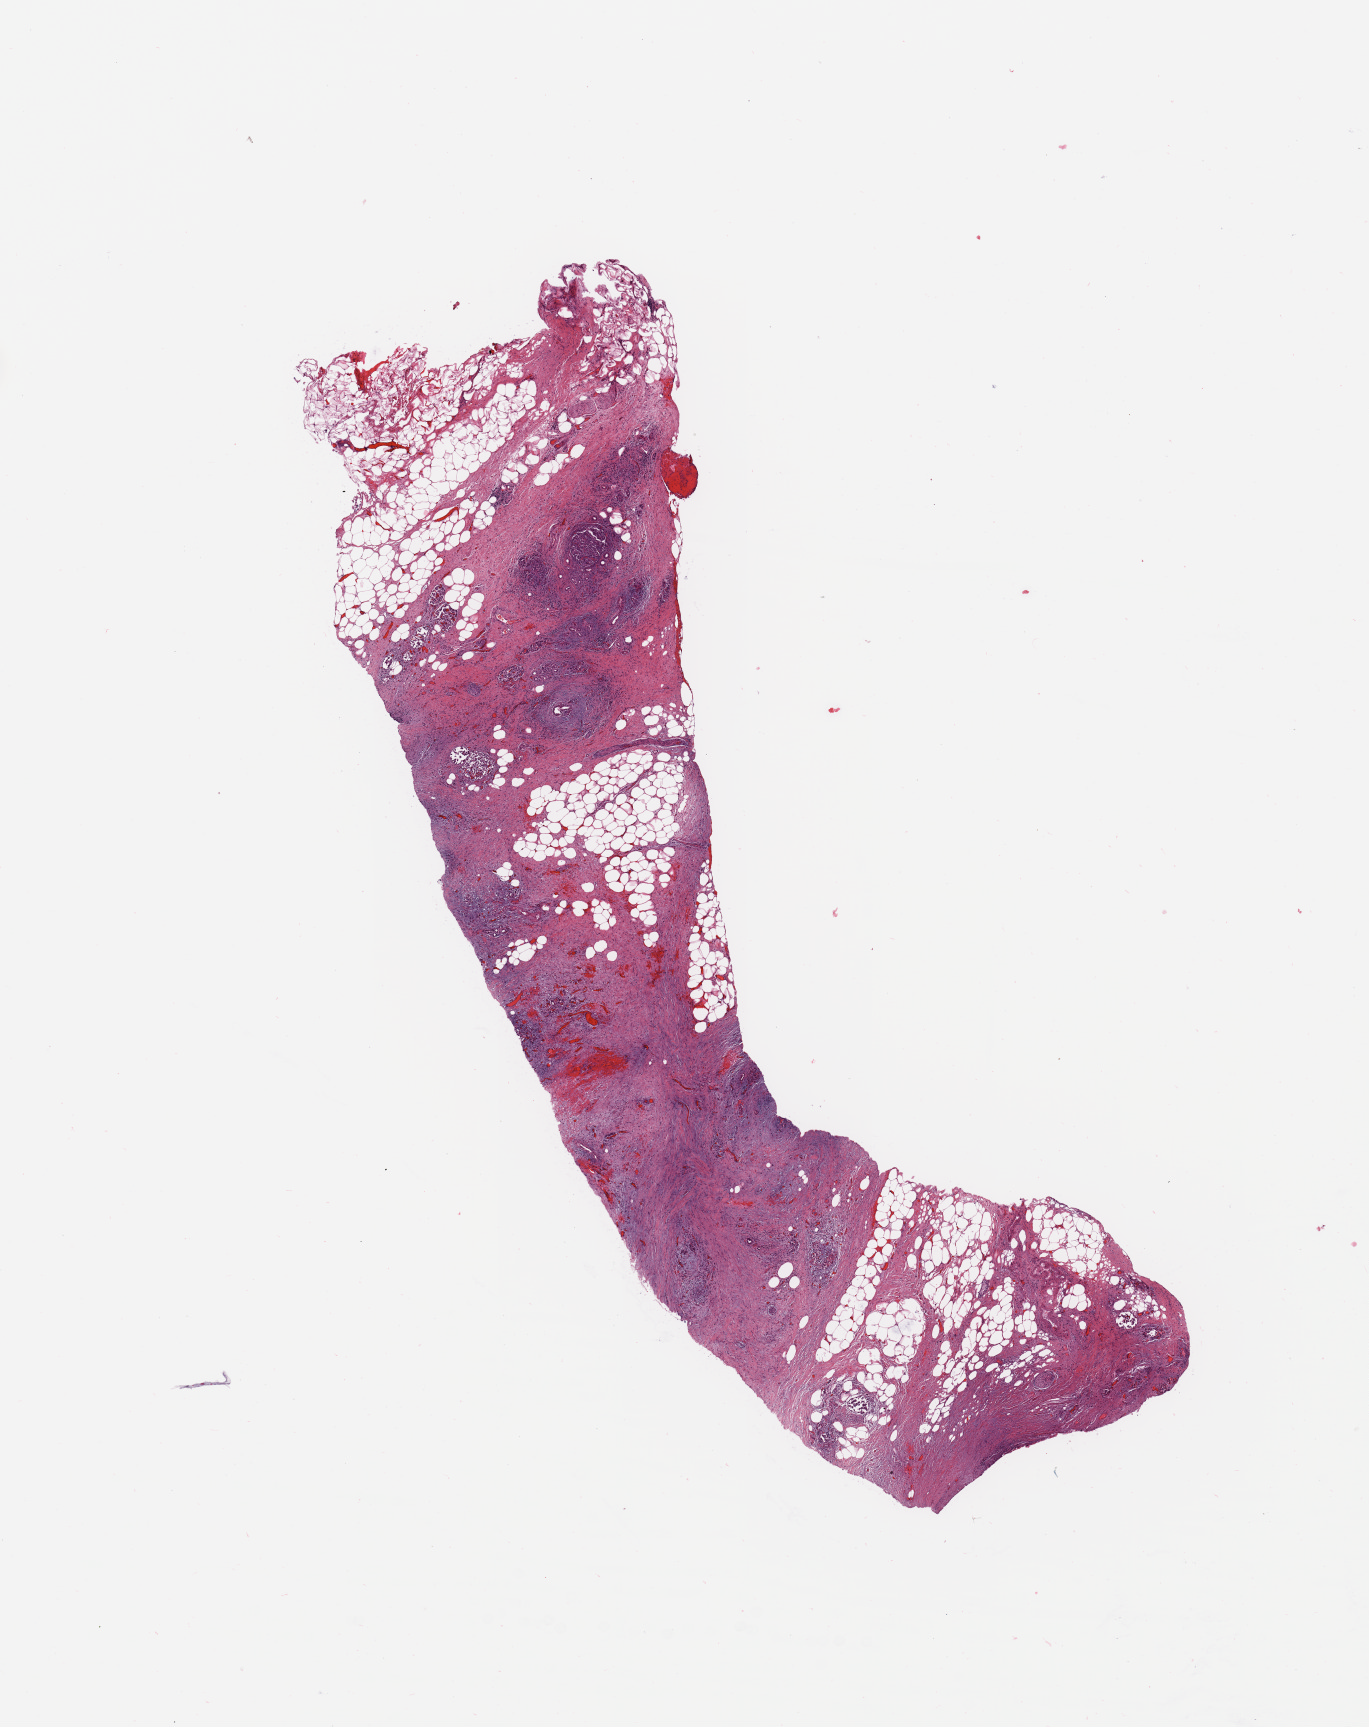
Hematoxylin and eosin (H&E) stained whole-slide image, a low-resolution overview of the entire scanned area, about 10.8 x 13.7 mm (from a 20x scan); pancreas, tissue type not recorded.
Patient diagnosis (cohort enrolment): ductal adenocarcinoma (pancreas).